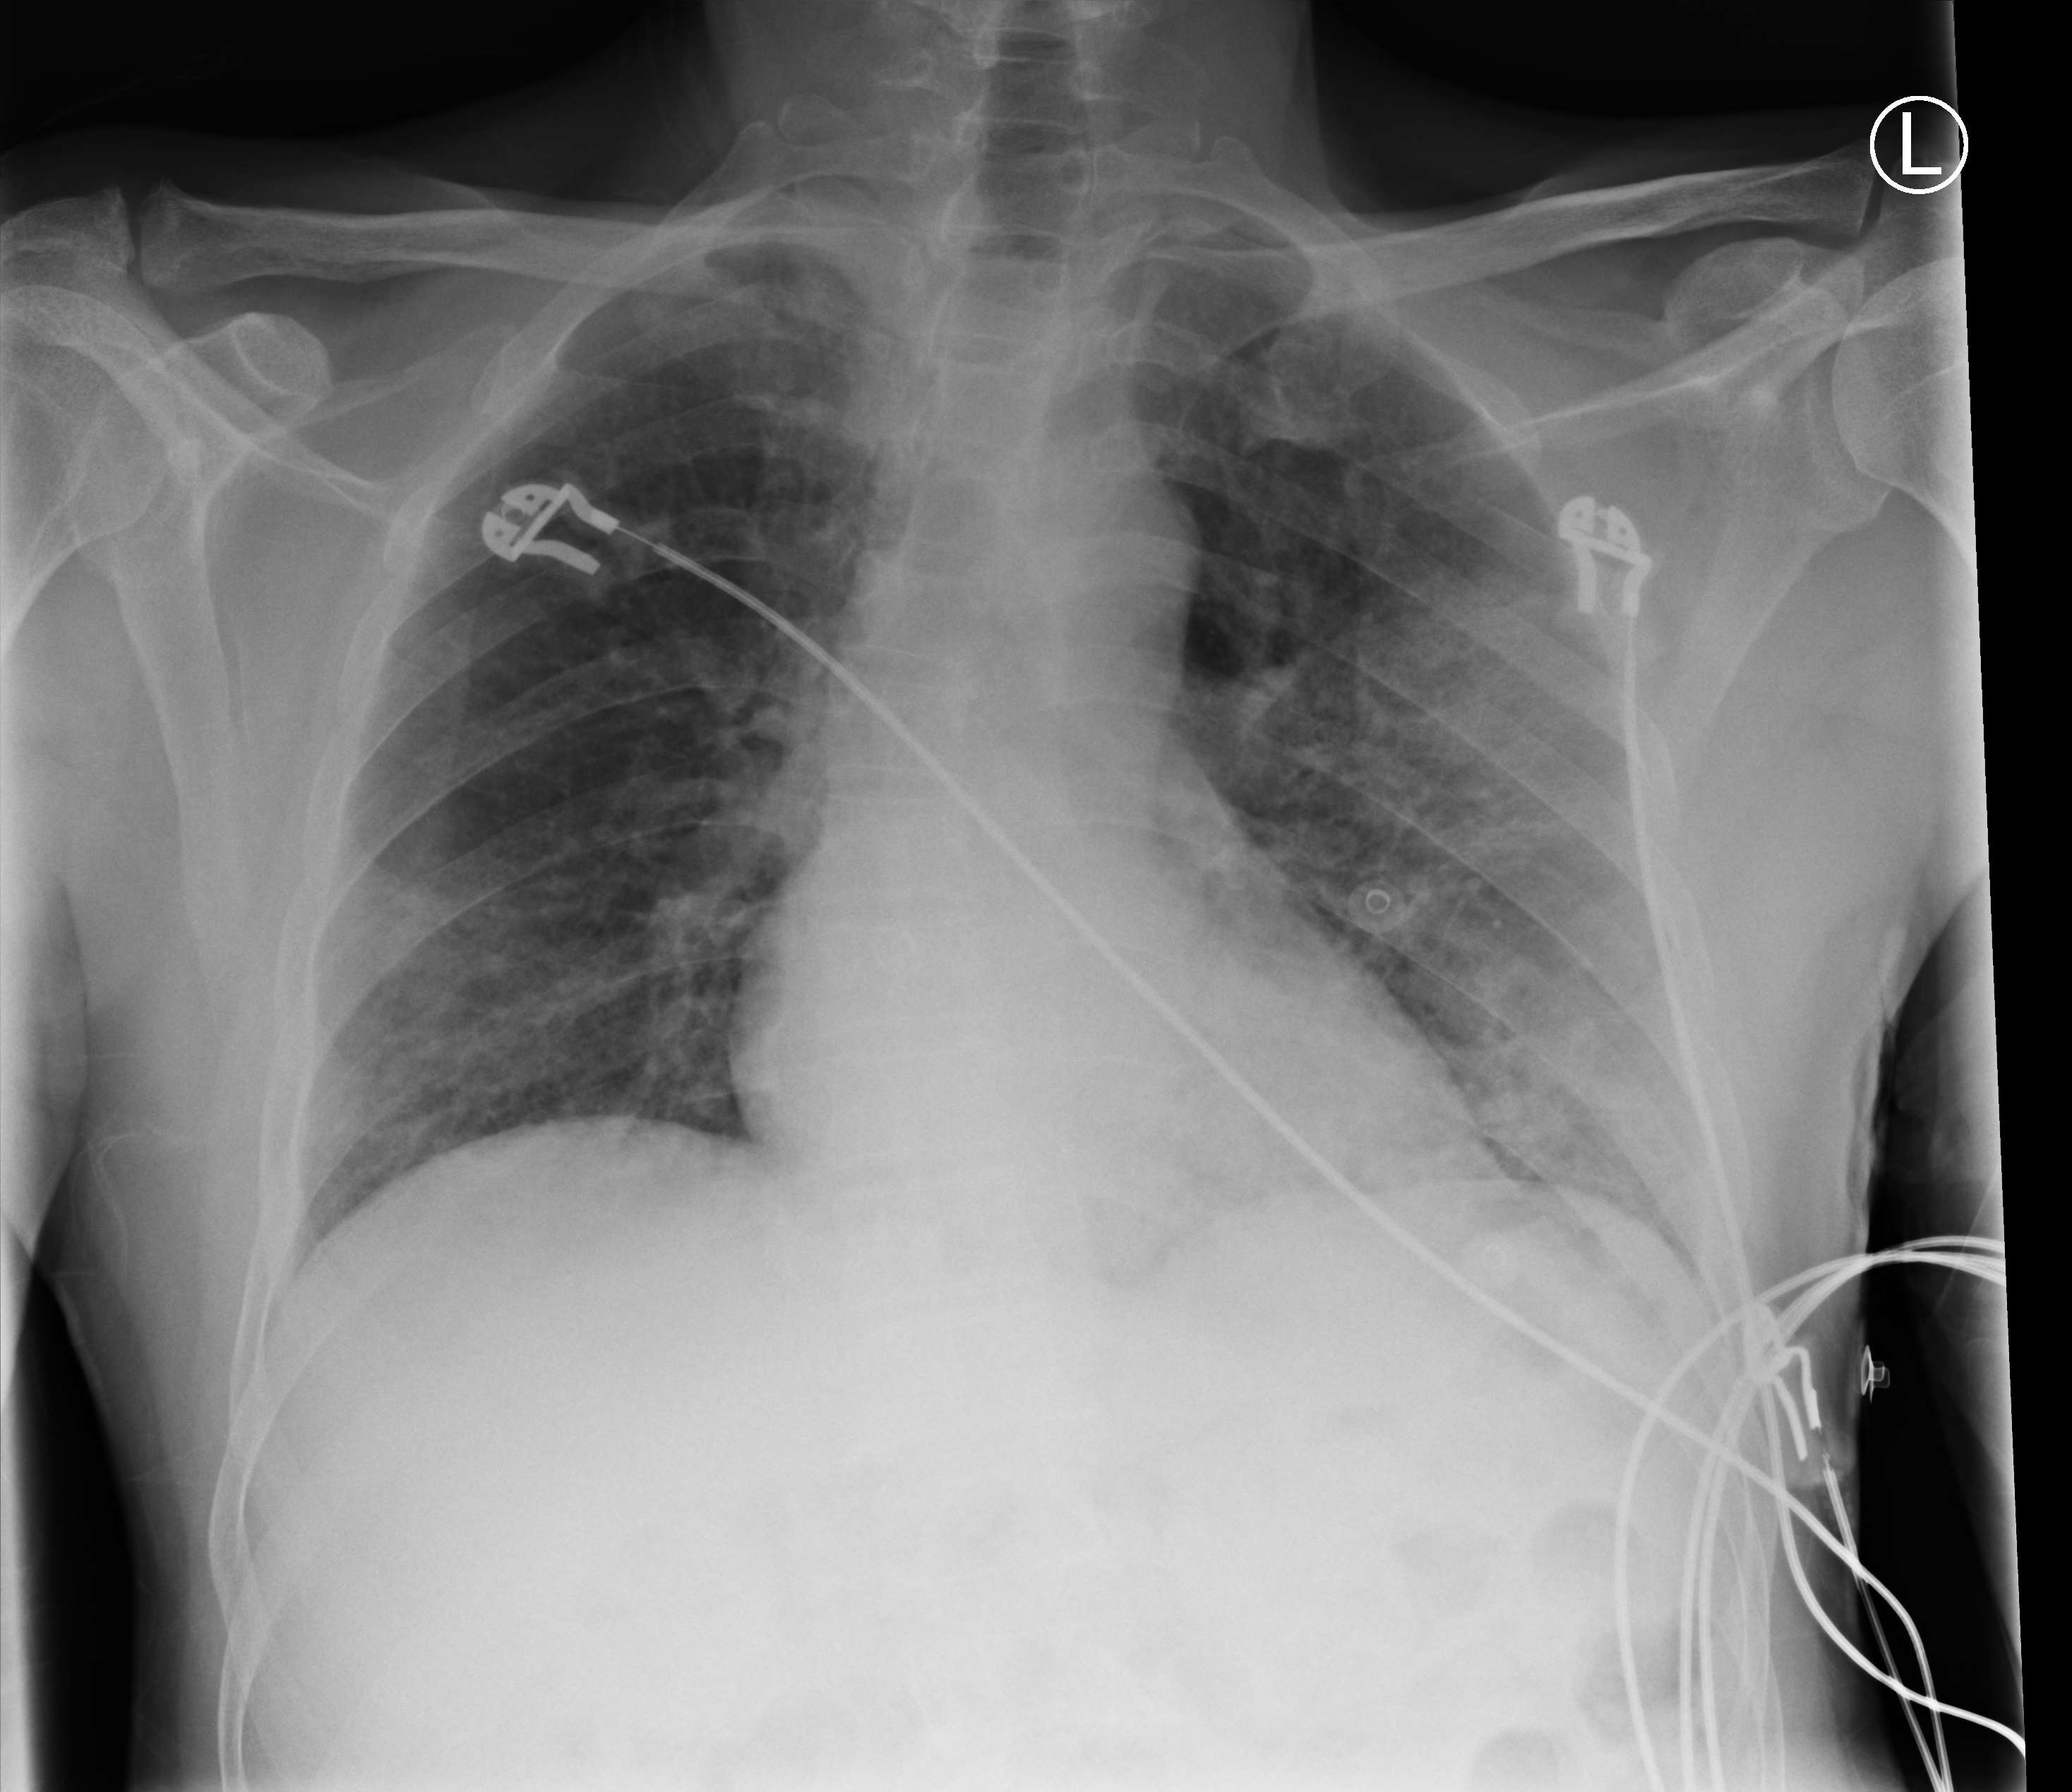
Portable chest radiograph, anteroposterior (AP) projection. Patient hospitalised with COVID-19; male, aged 60–74 years.
From the hospital-stay record, not from the radiograph (when in the stay this image was taken is not recorded):
- admitted to intensive care during this hospital stay: no